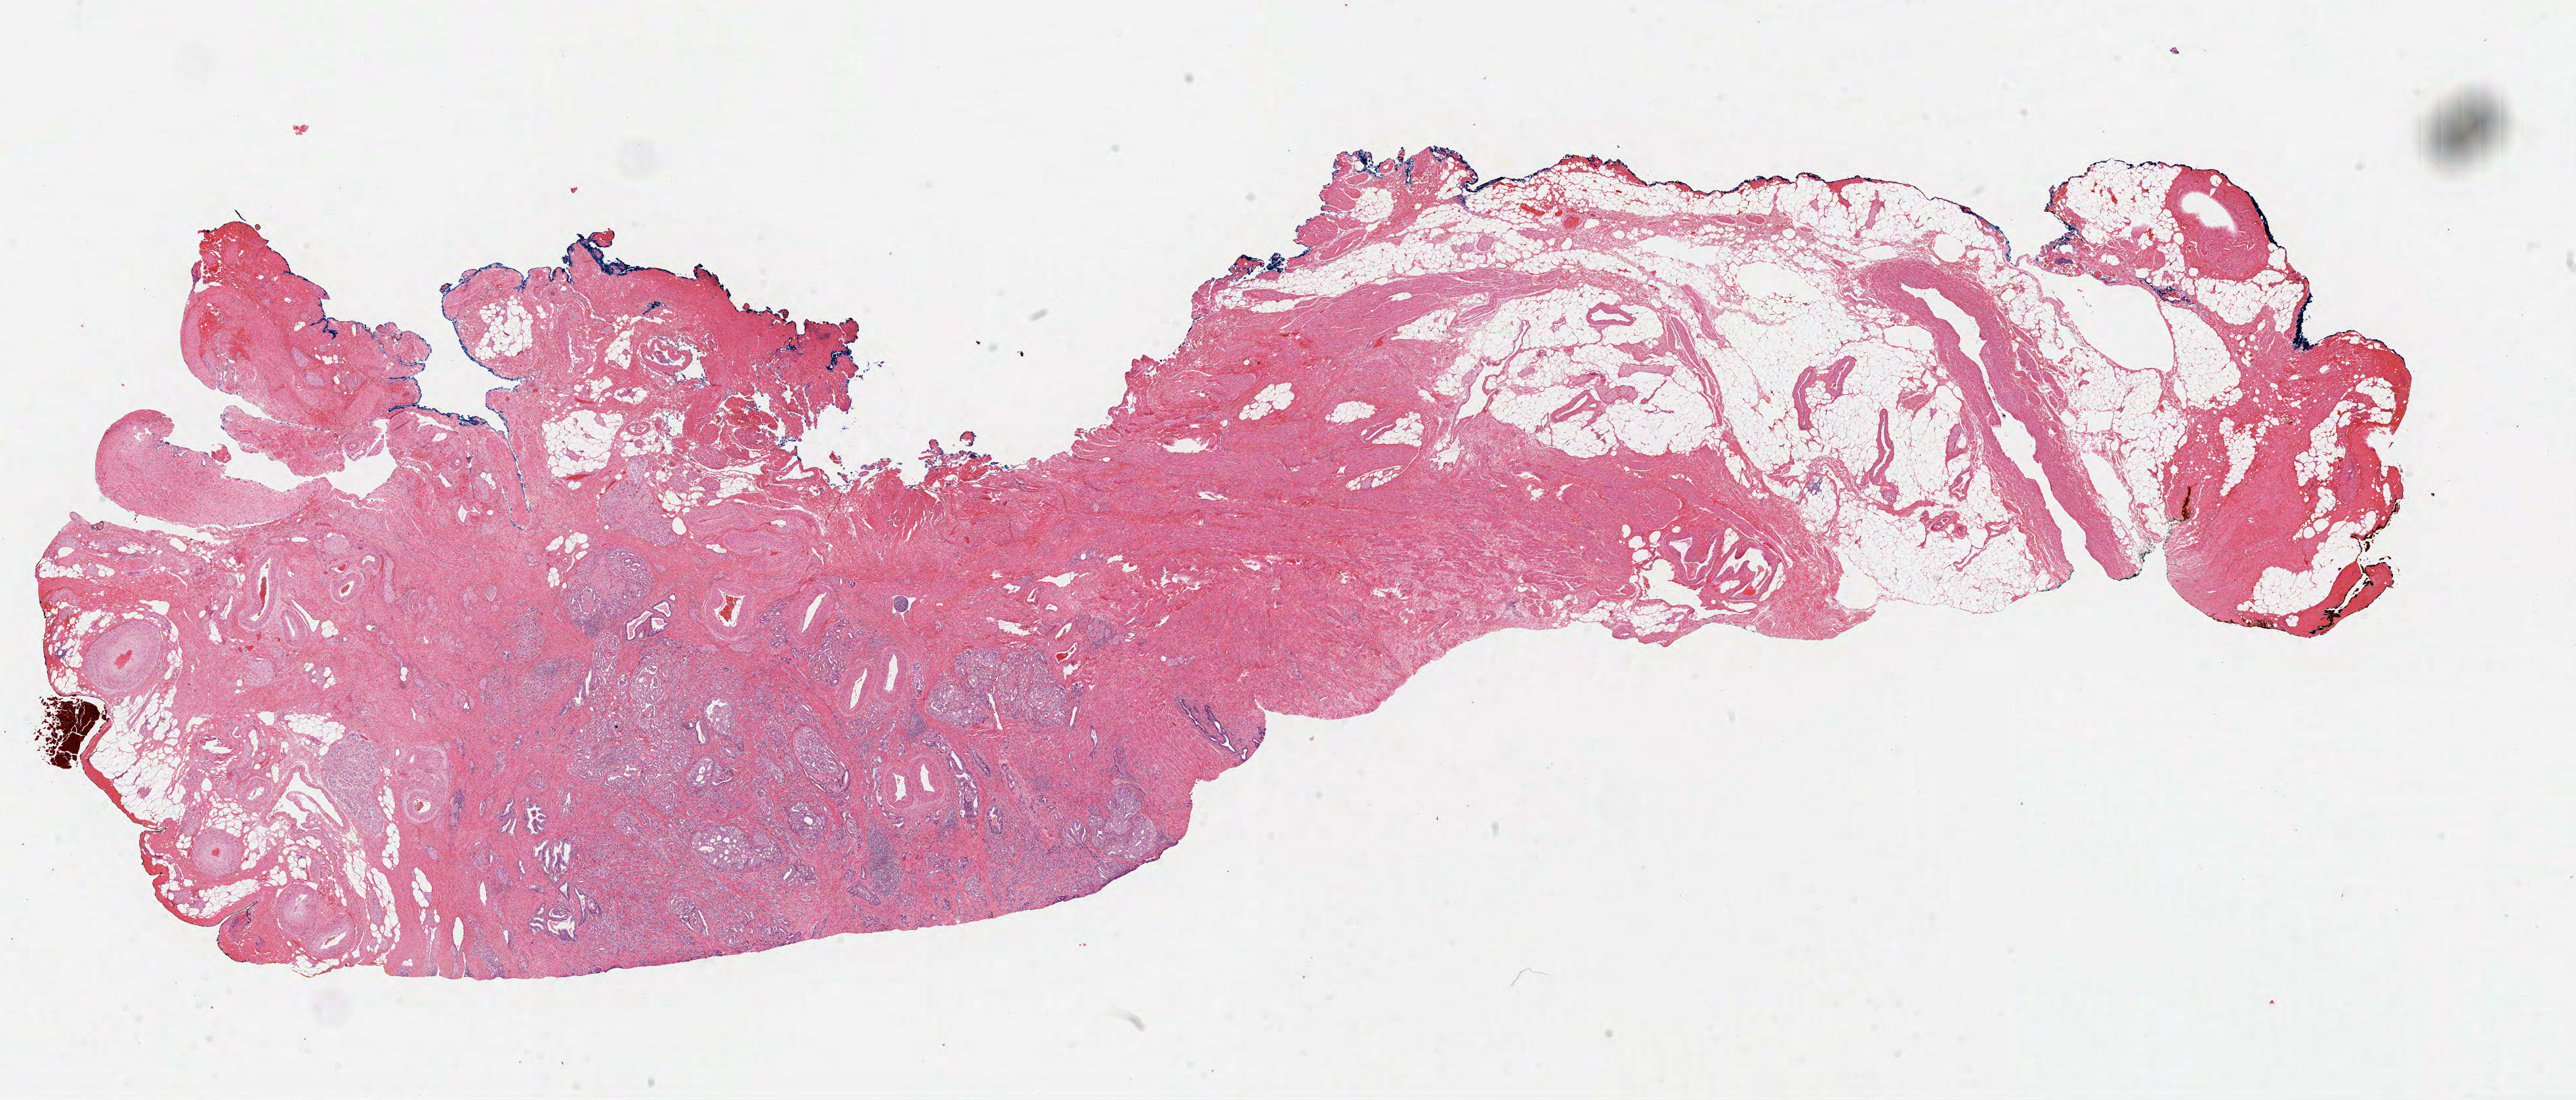
H&E-stained whole-slide image, a low-resolution overview of the entire scanned area, about 31.7 x 13.5 mm. FFPE section. Prostate, primary tumour sample. Male patient; age at initial diagnosis 68 years. Gleason score: 7 (4+3).
* pathologic diagnosis: Acinar cell carcinoma (prostate gland)